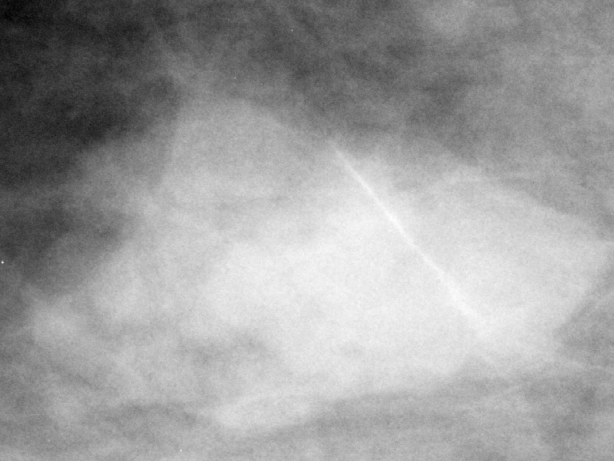
Region of interest cut from a scanned film mammogram (one marked finding), right breast, CC view, BI-RADS breast density category 2 (scale 1–4).
Marked abnormality: mass, shape lobulated, margins circumscribed; BI-RADS assessment category 4; pathology (as recorded): benign.